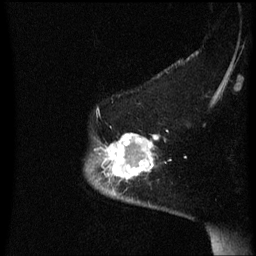
Breast MRI (dynamic contrast-enhanced), one sagittal slice; position 50 of 60 along the scan axis; dynamic contrast-enhanced series, image 2 of 3 at this slice position (ordered by acquisition); 1.5 T; TE 4.2 ms, TR 8.4 ms; 256 × 256 image matrix, field of view 200 × 200 mm. Patient: female, 54 years. Case-level facts recorded for this patient, not image findings: setting: breast cancer imaged before/during neoadjuvant chemotherapy; receptor status: HR-positive, HER2-negative.
Annotated regions visible in this slice (semi-automatic segmentation, software-assisted and operator-edited):
- analysis volume of interest (the breast-tissue region the enhancement analysis was run in; not a lesion): box from (x=95, y=134) to (x=160, y=191) px
- tumour enhancement mask (voxels above the 70 % enhancement threshold inside the analysis volume of interest): (x=105, y=134)–(x=160, y=183)